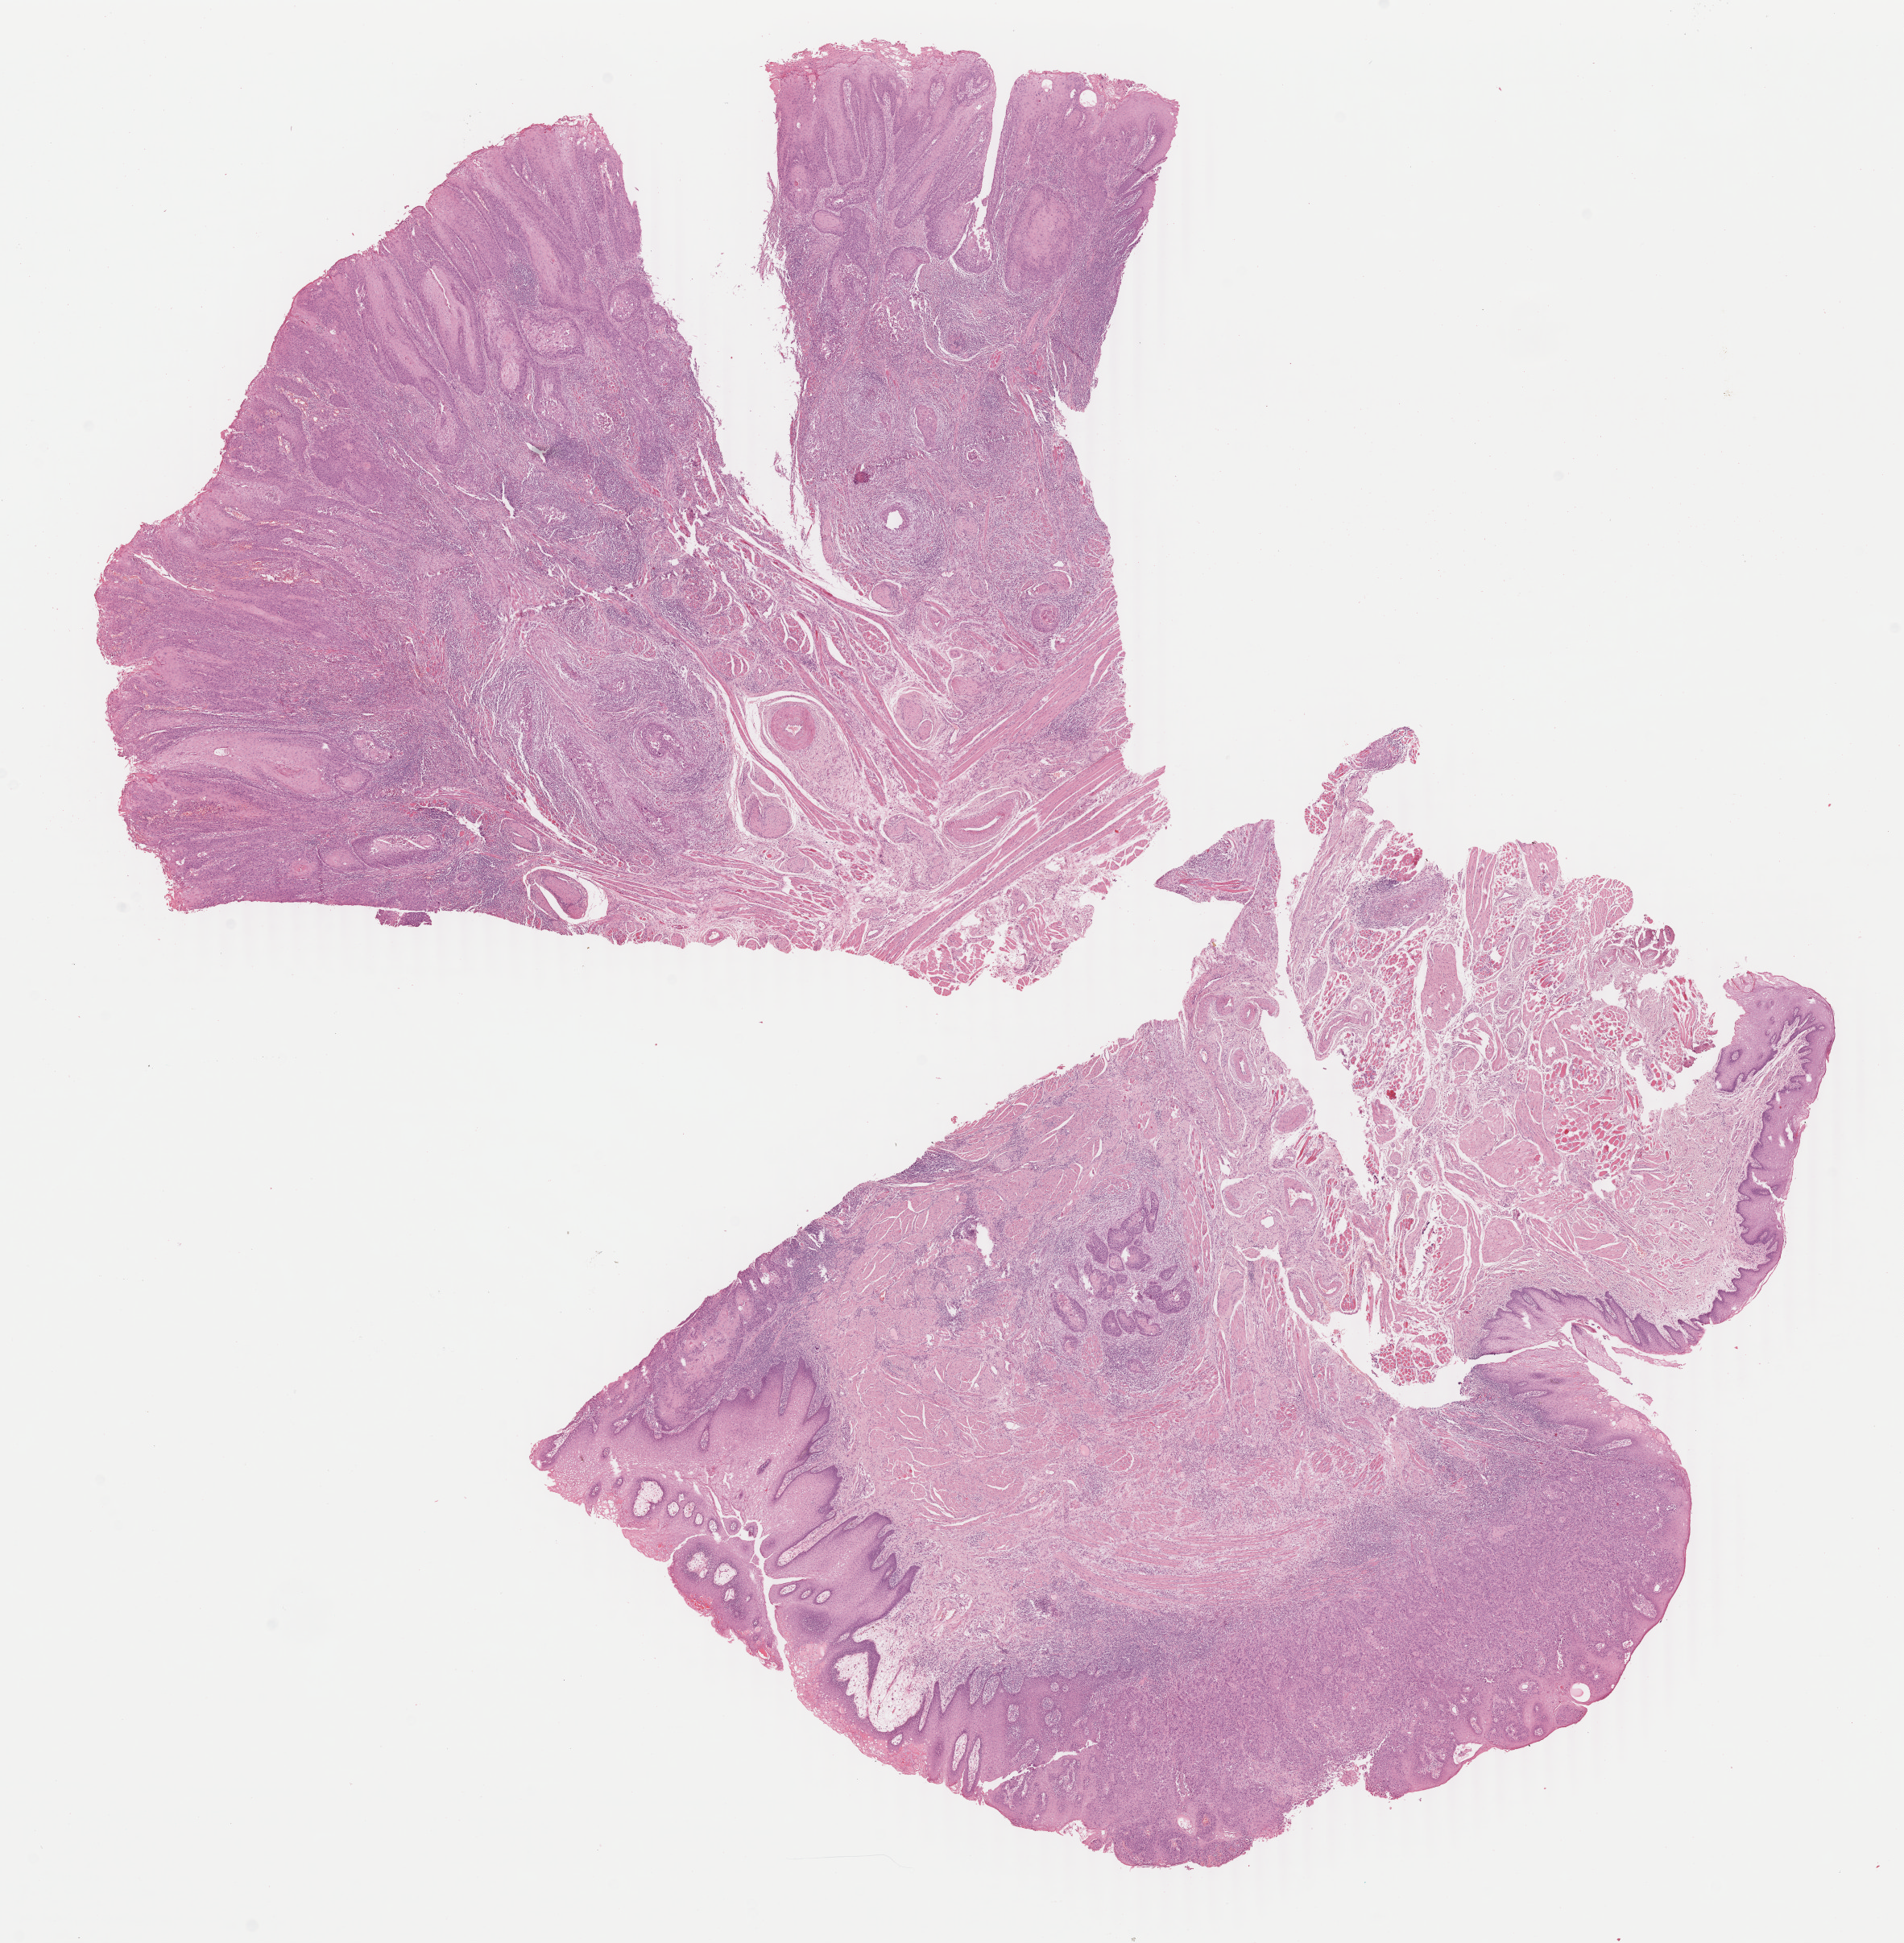
Whole-slide histology image, H&E, shown as a low-resolution overview of the whole scanned area (about 18.8 x 19.2 mm, acquisition: 40x scan); formalin-fixed paraffin-embedded (FFPE) diagnostic section; head and neck, primary tumour sample. Male patient; age at initial diagnosis 52 years. Histologic grade: G2 (moderately differentiated).
Histologic diagnosis: Squamous cell carcinoma, keratinizing, NOS (tongue, NOS). Laterality: midline. AJCC pathologic stage: II.